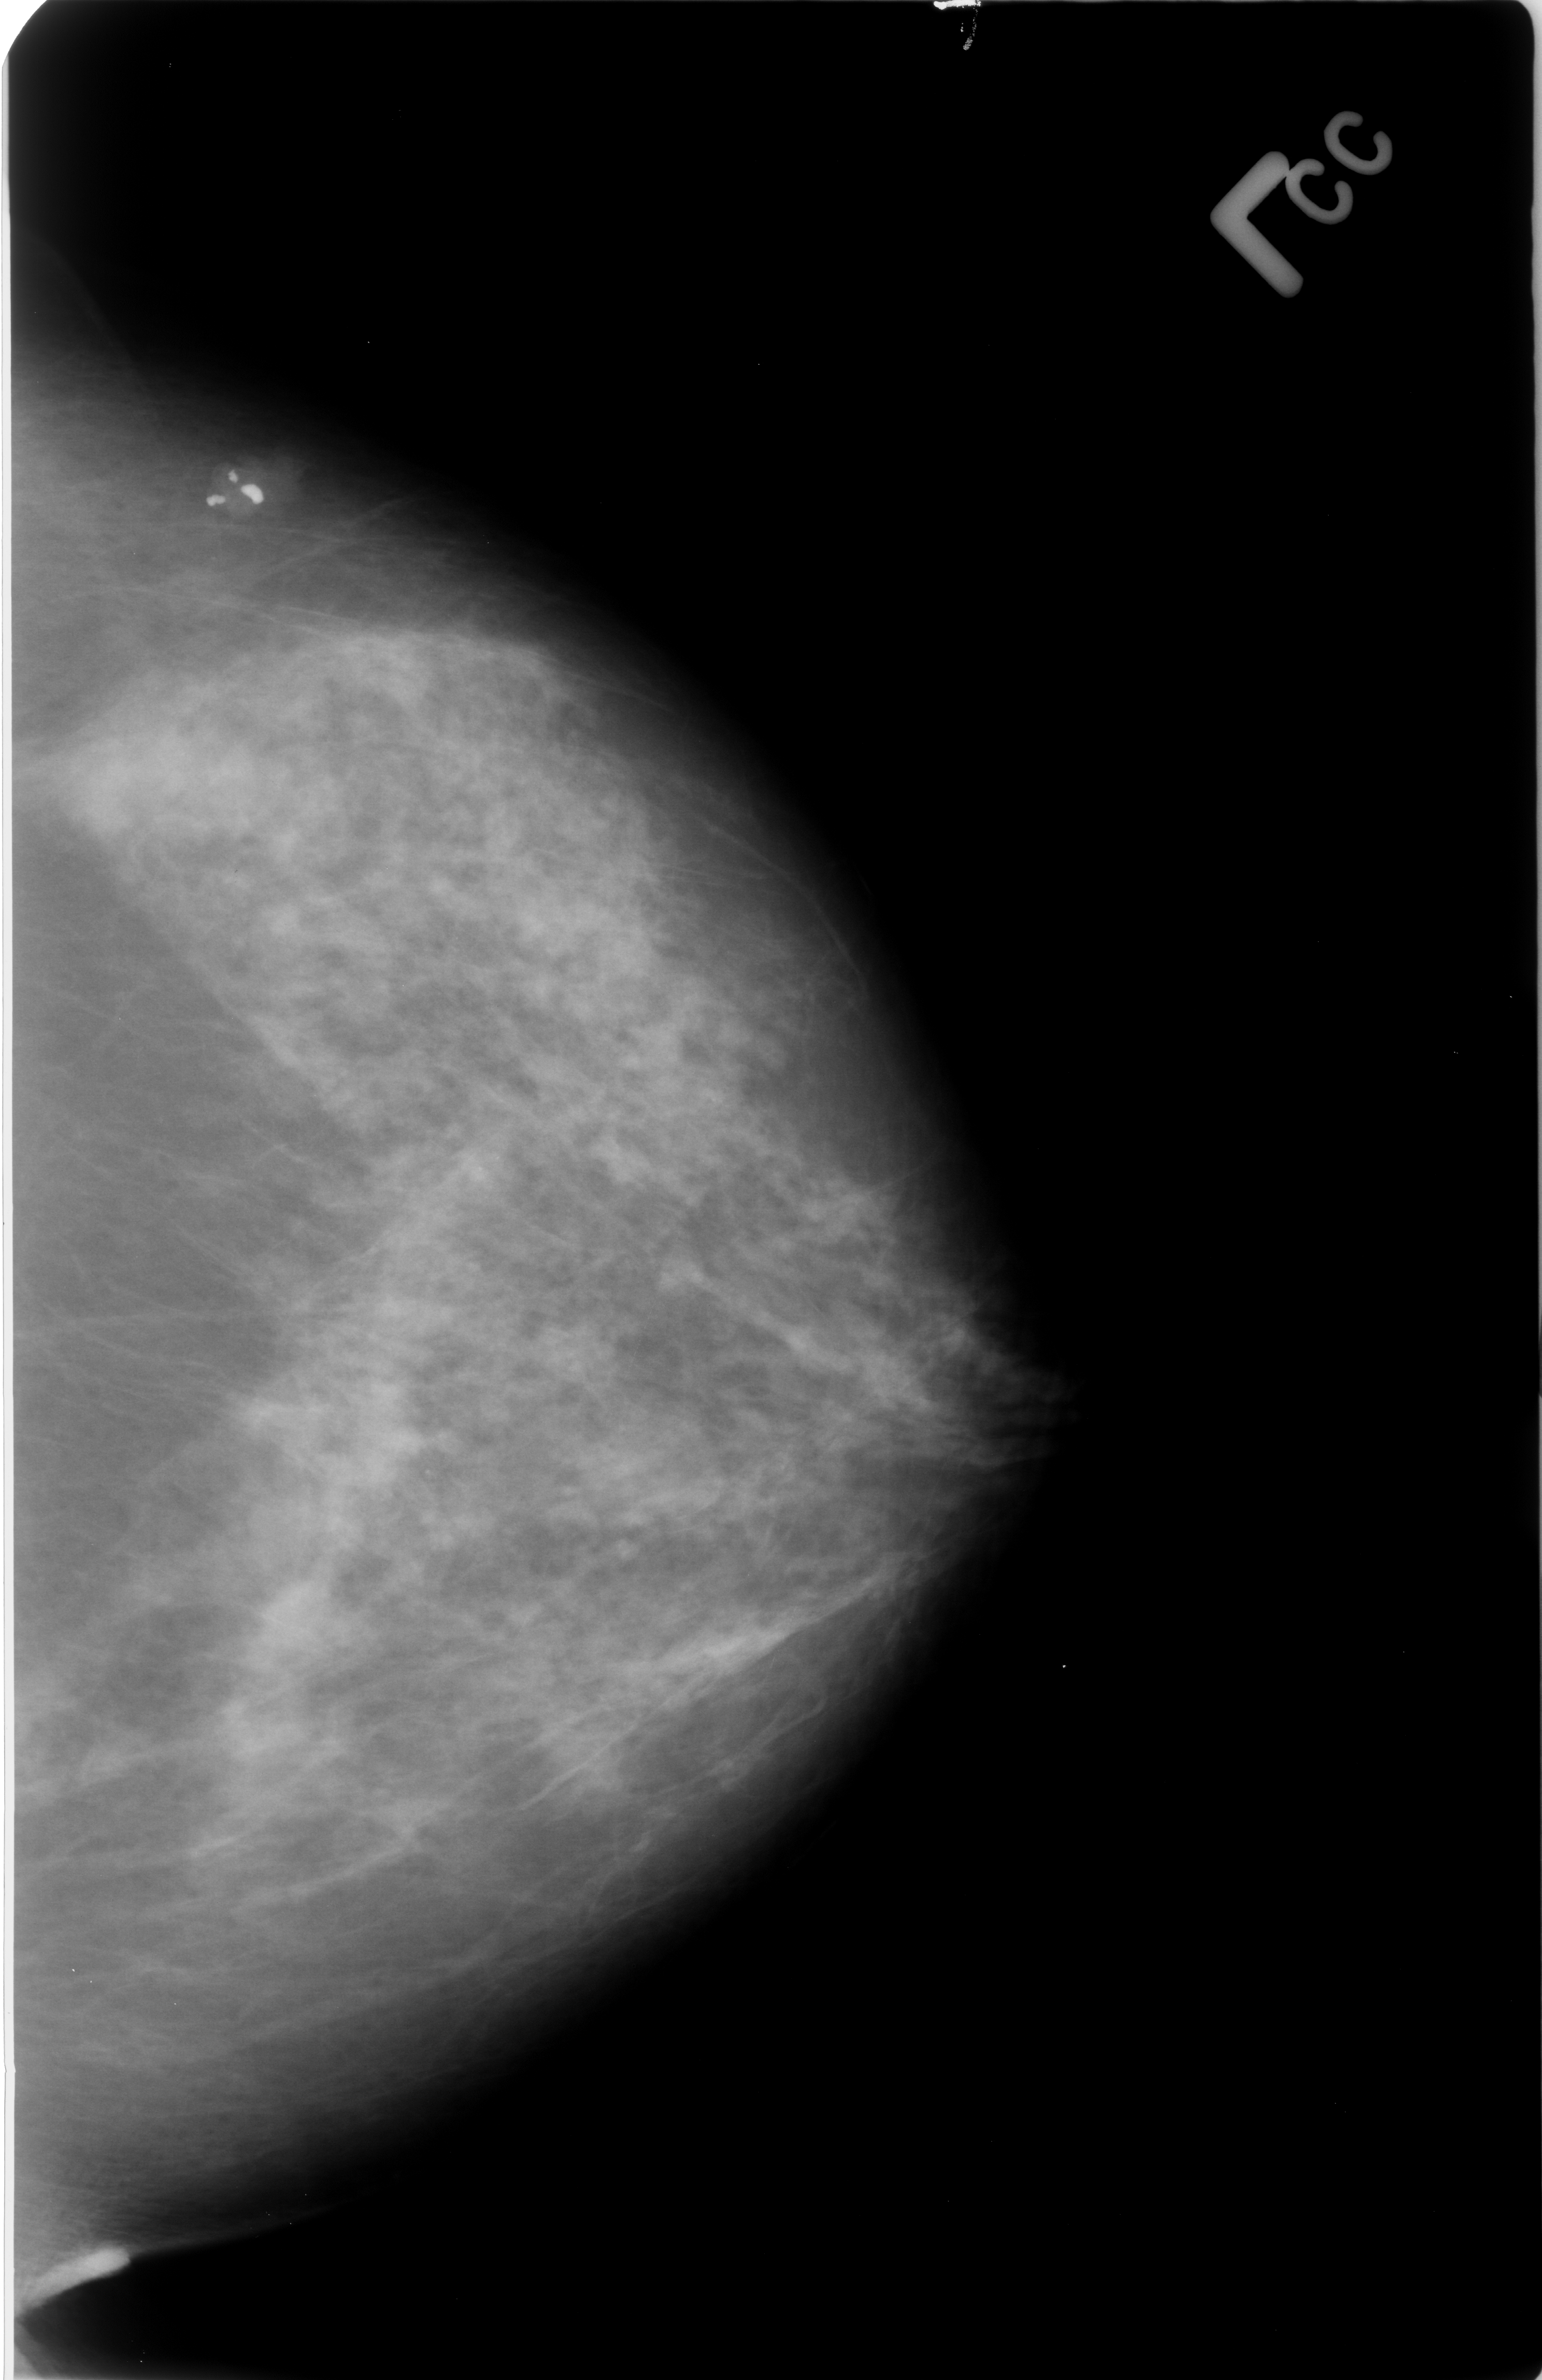
Digitized screen-film mammogram; left breast; craniocaudal (CC) view; BI-RADS breast density category 3 (scale 1–4).
Radiologist-marked abnormalities on this image: calcifications, morphology coarse; BI-RADS assessment category 2; benign; no additional work-up was recommended (benign without callback).